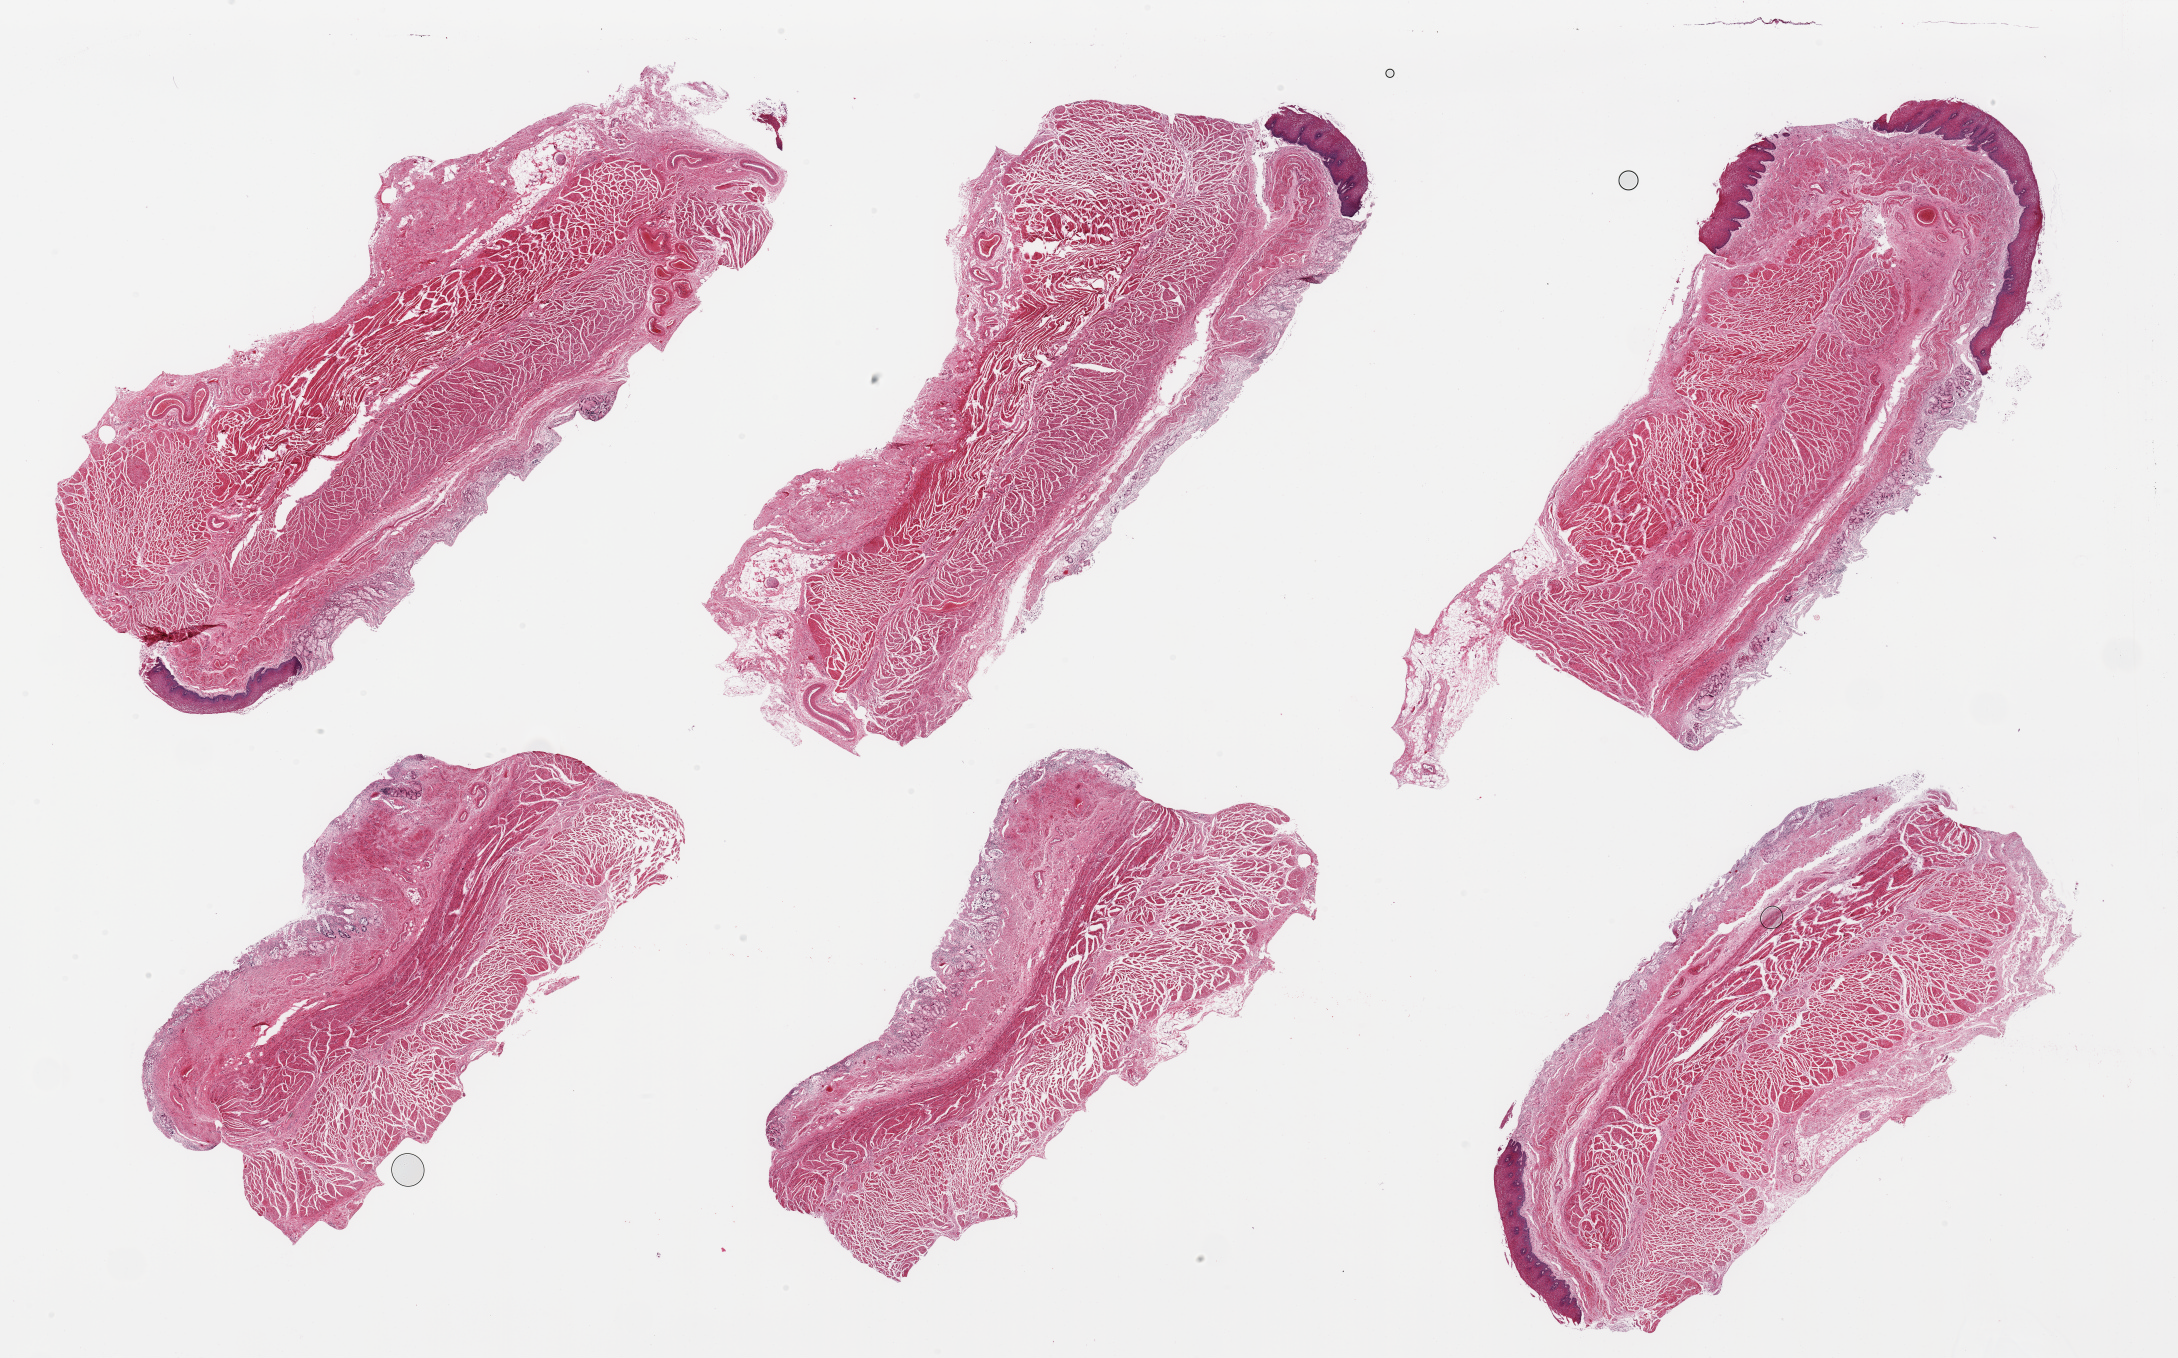
Hematoxylin and eosin (H&E) whole-slide image, whole scanned area (about 34.5 x 21.5 mm, acquisition: 20x scan) shown as a low-resolution overview; PAXgene-fixed, paraffin-embedded tissue; sampled site (target tissue): gastroesophageal junction; tissue donor sample.
Review note (as recorded): 6 pieces; target muscularis present; small fragments of squamous epithelium and severely autolyzed glandular mucosa; ~2mm of serosa and fat.